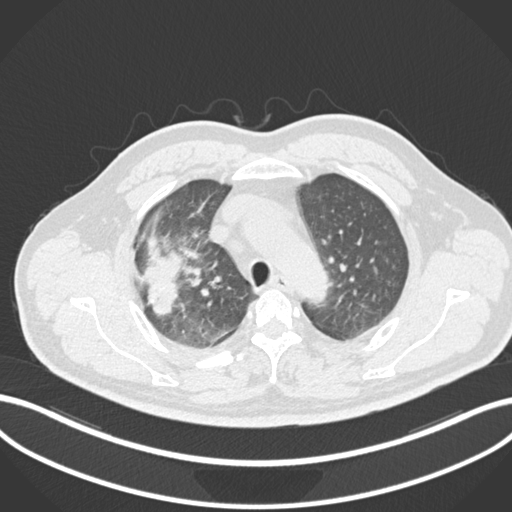
Chest CT, one axial slice; slice 677 of 852 in the series (ordered by position); reconstruction kernel B30f; lung window (W 1500 / L -600 HU); 1 mm slice thickness; 512 × 512 image matrix. Patient: male, 55 years. Case-level facts recorded for this patient, not image findings: clinical TNM (as recorded): T3 N2 M1.
Outlined on this slice (bounding box drawn by a radiologist):
- lung tumour (recorded histology: adenocarcinoma): bounding box (x1, y1, x2, y2) in pixels: (143, 236, 185, 320)